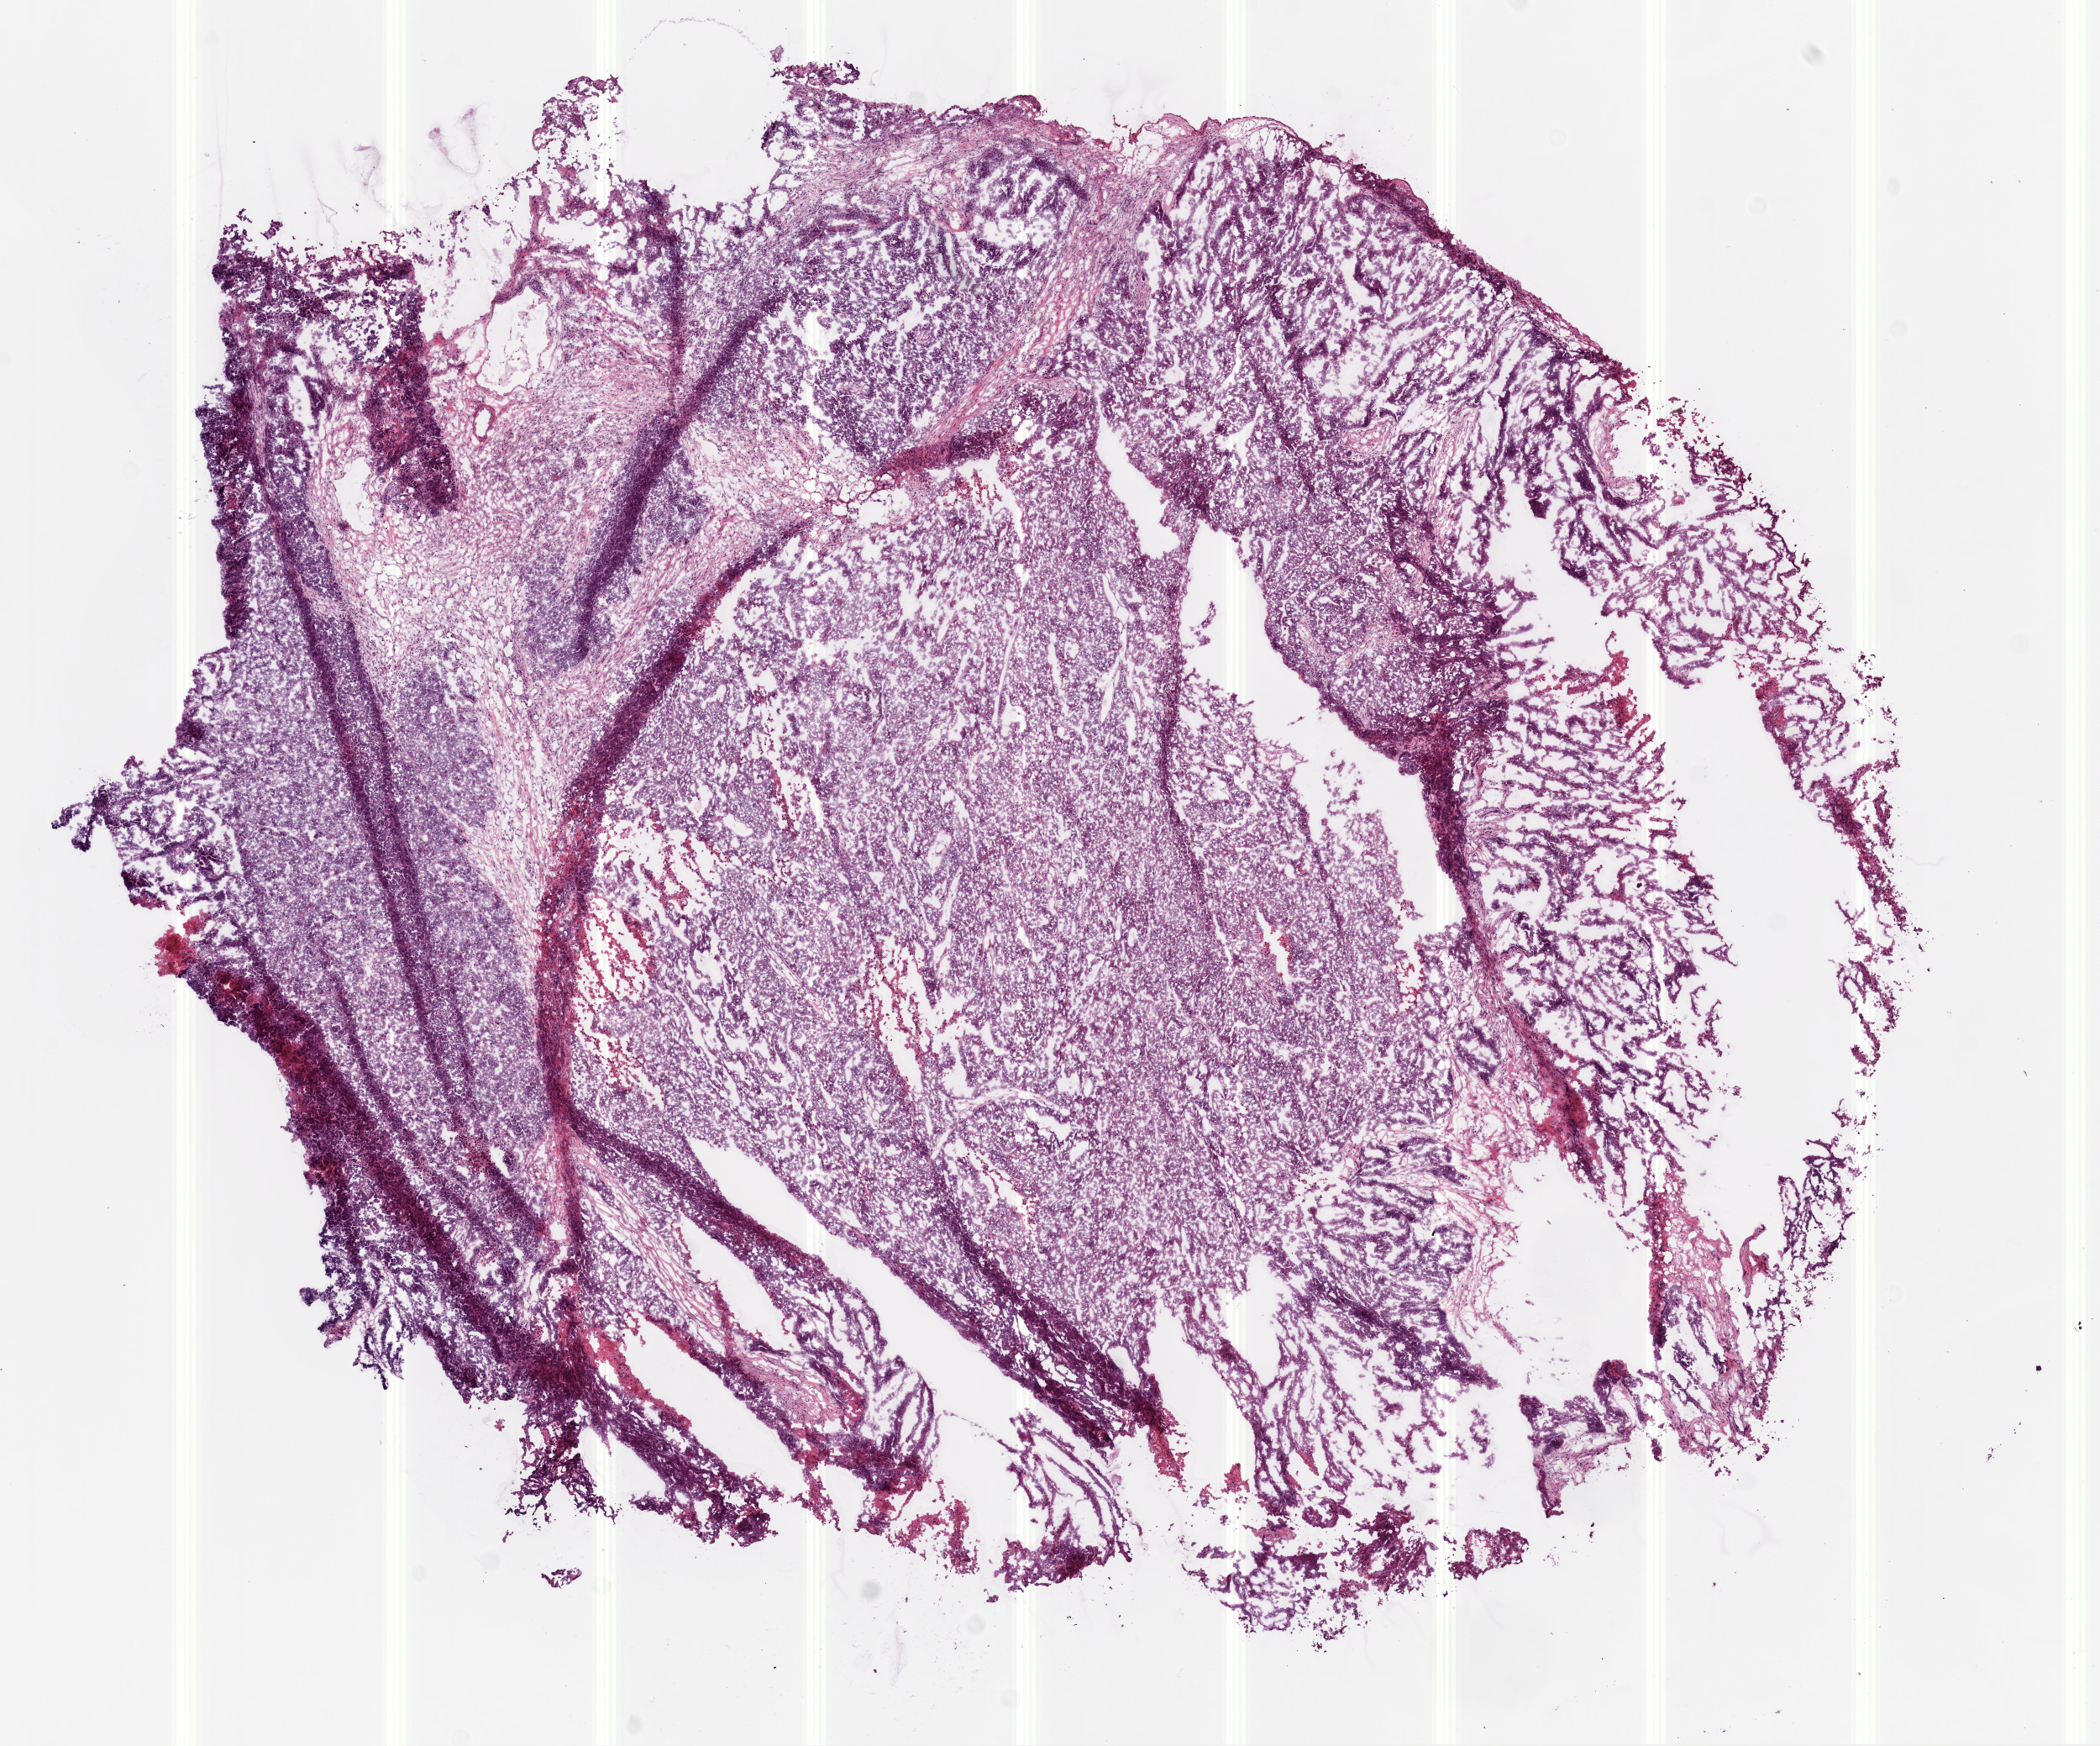
Whole-slide histology image, Hematoxylin and eosin (H&E) stained — shown as a low-resolution overview of the whole scanned area (about 10.0 x 8.3 mm, acquisition: 20x scan). Frozen section from the bottom of the tissue portion. Sample: primary tumour, ovary. Patient: female, age at initial diagnosis 80 years. Histologic grade: G3 (poorly differentiated). Composition of this section per pathologist review: tumour cells 90%, tumour nuclei 75%, normal cells 0%, stromal cells 5%, necrosis 5%. Infiltration values recorded for this section: lymphocyte infiltration 15%.
* diagnosis: Serous cystadenocarcinoma, NOS
* FIGO stage: IIIC